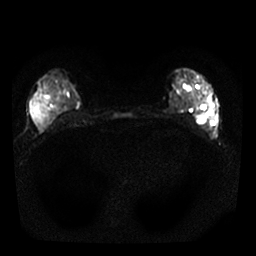
Breast MRI, one axial slice. Slice 13 of 25 in the series (ordered by position). Diffusion-weighted series; image 2 of 4 stored at this slice position (different b-values; order by instance number). 1.5 T. 4 mm slice thickness. 256 × 256 image matrix, field of view 290 × 290 mm. Female patient.
Structures marked on this image (outlined manually by an expert reader):
- tumour on diffusion-weighted imaging: bounding box [x1, y1, x2, y2] px = [57, 78, 73, 92]